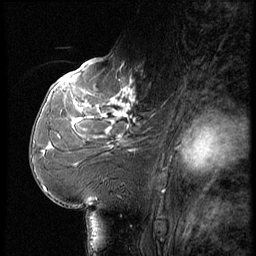
Breast MRI (dynamic contrast-enhanced), one sagittal slice. Position 33 of 56 along the scan axis. Dynamic contrast-enhanced series, image 2 of 3 at this slice position (ordered by acquisition). 1.5 T. TE 4.2 ms, TR 9 ms. 2.5 mm slice thickness. 256 × 256 image matrix, field of view 180 × 180 mm. Female patient, age 61 years. From the clinical record (not read from this slice): setting: breast cancer imaged before/during neoadjuvant chemotherapy; receptor status: HR-positive, HER2-negative.
Outlined on this slice (semi-automatically segmented with operator editing):
- analysis volume of interest (the breast-tissue region the enhancement analysis was run in; not a lesion): bounding box (x1, y1, x2, y2) in pixels: (65, 74, 153, 175)
- tumour enhancement mask (voxels above the 140 % enhancement threshold inside the analysis volume of interest): (74, 87, 135, 126)